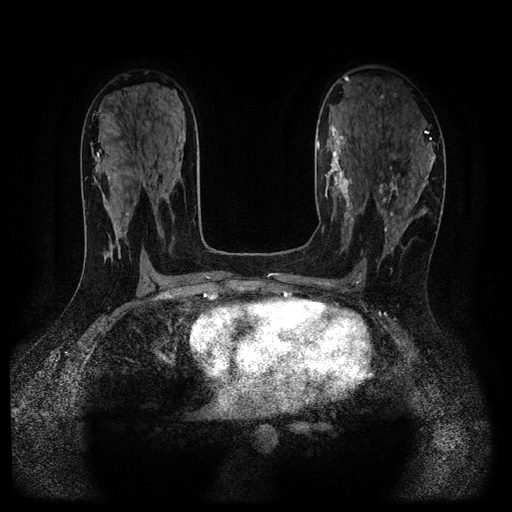
Breast MRI (dynamic contrast-enhanced, multi-phase), one axial slice. Slice 61 of 116 in the series (ordered by position). Dynamic contrast-enhanced series, time point 2 of 5 at this slice position (early post-contrast). 1.5 T. TE 2.7 ms, TR 5.4 ms. 2.2 mm slice thickness. 512 × 512 image matrix. Patient: female, 43 years.
Annotated regions visible in this slice (semi-automatically segmented with operator editing):
- breast lesion (labelled 'tumour' in the annotation; benign lesions carry a separate 'benign' label): bounding box (x1, y1, x2, y2) in pixels: (375, 177, 399, 209)
- breast lesion (labelled benign in the annotation): (320, 125, 358, 234)